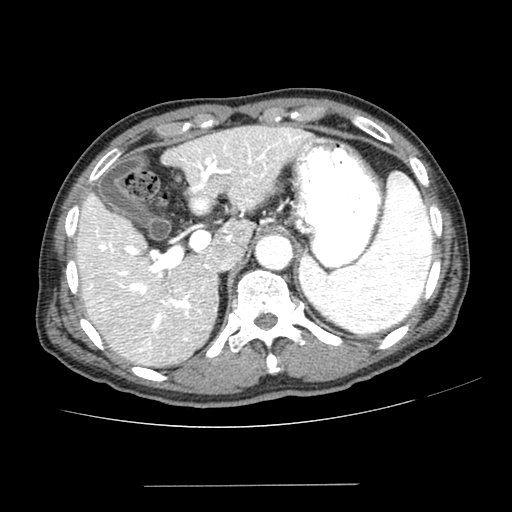
Contrast-enhanced abdominal CT (liver protocol), one axial slice. Slice 160 of 187 in the series (ordered by position). Reconstruction kernel SOFT. 100 kVp. One of 2 acquisitions stored at this slice position. Soft-tissue window (W 400 / L 40 HU). 512 × 512 image matrix. From the clinical record (not read from this slice): diagnosis: hepatocellular carcinoma (patient treated with transarterial chemoembolisation; whether this scan precedes or follows treatment is not stated here); TNM stage (as recorded): Stage-I; Child-Pugh class: A; tumour nodularity: uninodular; tumour size: 1.6 cm.
Annotated regions visible in this slice (semi-automatic segmentation, software-assisted and operator-edited):
- liver parenchyma outside the tumour (the mass and vessels are separate outlines, so this box may not span the whole liver): box from (x=76, y=126) to (x=312, y=366) px
- liver vessels: (x=87, y=132)–(x=301, y=352)